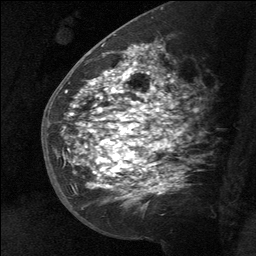
Breast MRI (dynamic contrast-enhanced), one sagittal slice. Position 36 of 64 along the scan axis. Dynamic contrast-enhanced study with each time point stored as its own series, time point 2 of 3 at this slice position (early post-contrast, ordered by acquisition time). 1.5 T. TE 4.8 ms, TR 27 ms. 256 × 256 image matrix, field of view 180 × 180 mm. Female patient, age 39 years. From the clinical record (not read from this slice): setting: breast cancer imaged before/during neoadjuvant chemotherapy; receptor status: HER2-positive.
Annotated regions visible in this slice (semi-automatically segmented with operator editing):
- analysis volume of interest (the breast-tissue region the enhancement analysis was run in; not a lesion): bounding box (x1, y1, x2, y2) in pixels: (58, 40, 165, 216)
- tumour enhancement mask (voxels above the 90 % enhancement threshold inside the analysis volume of interest): (68, 46, 155, 197)